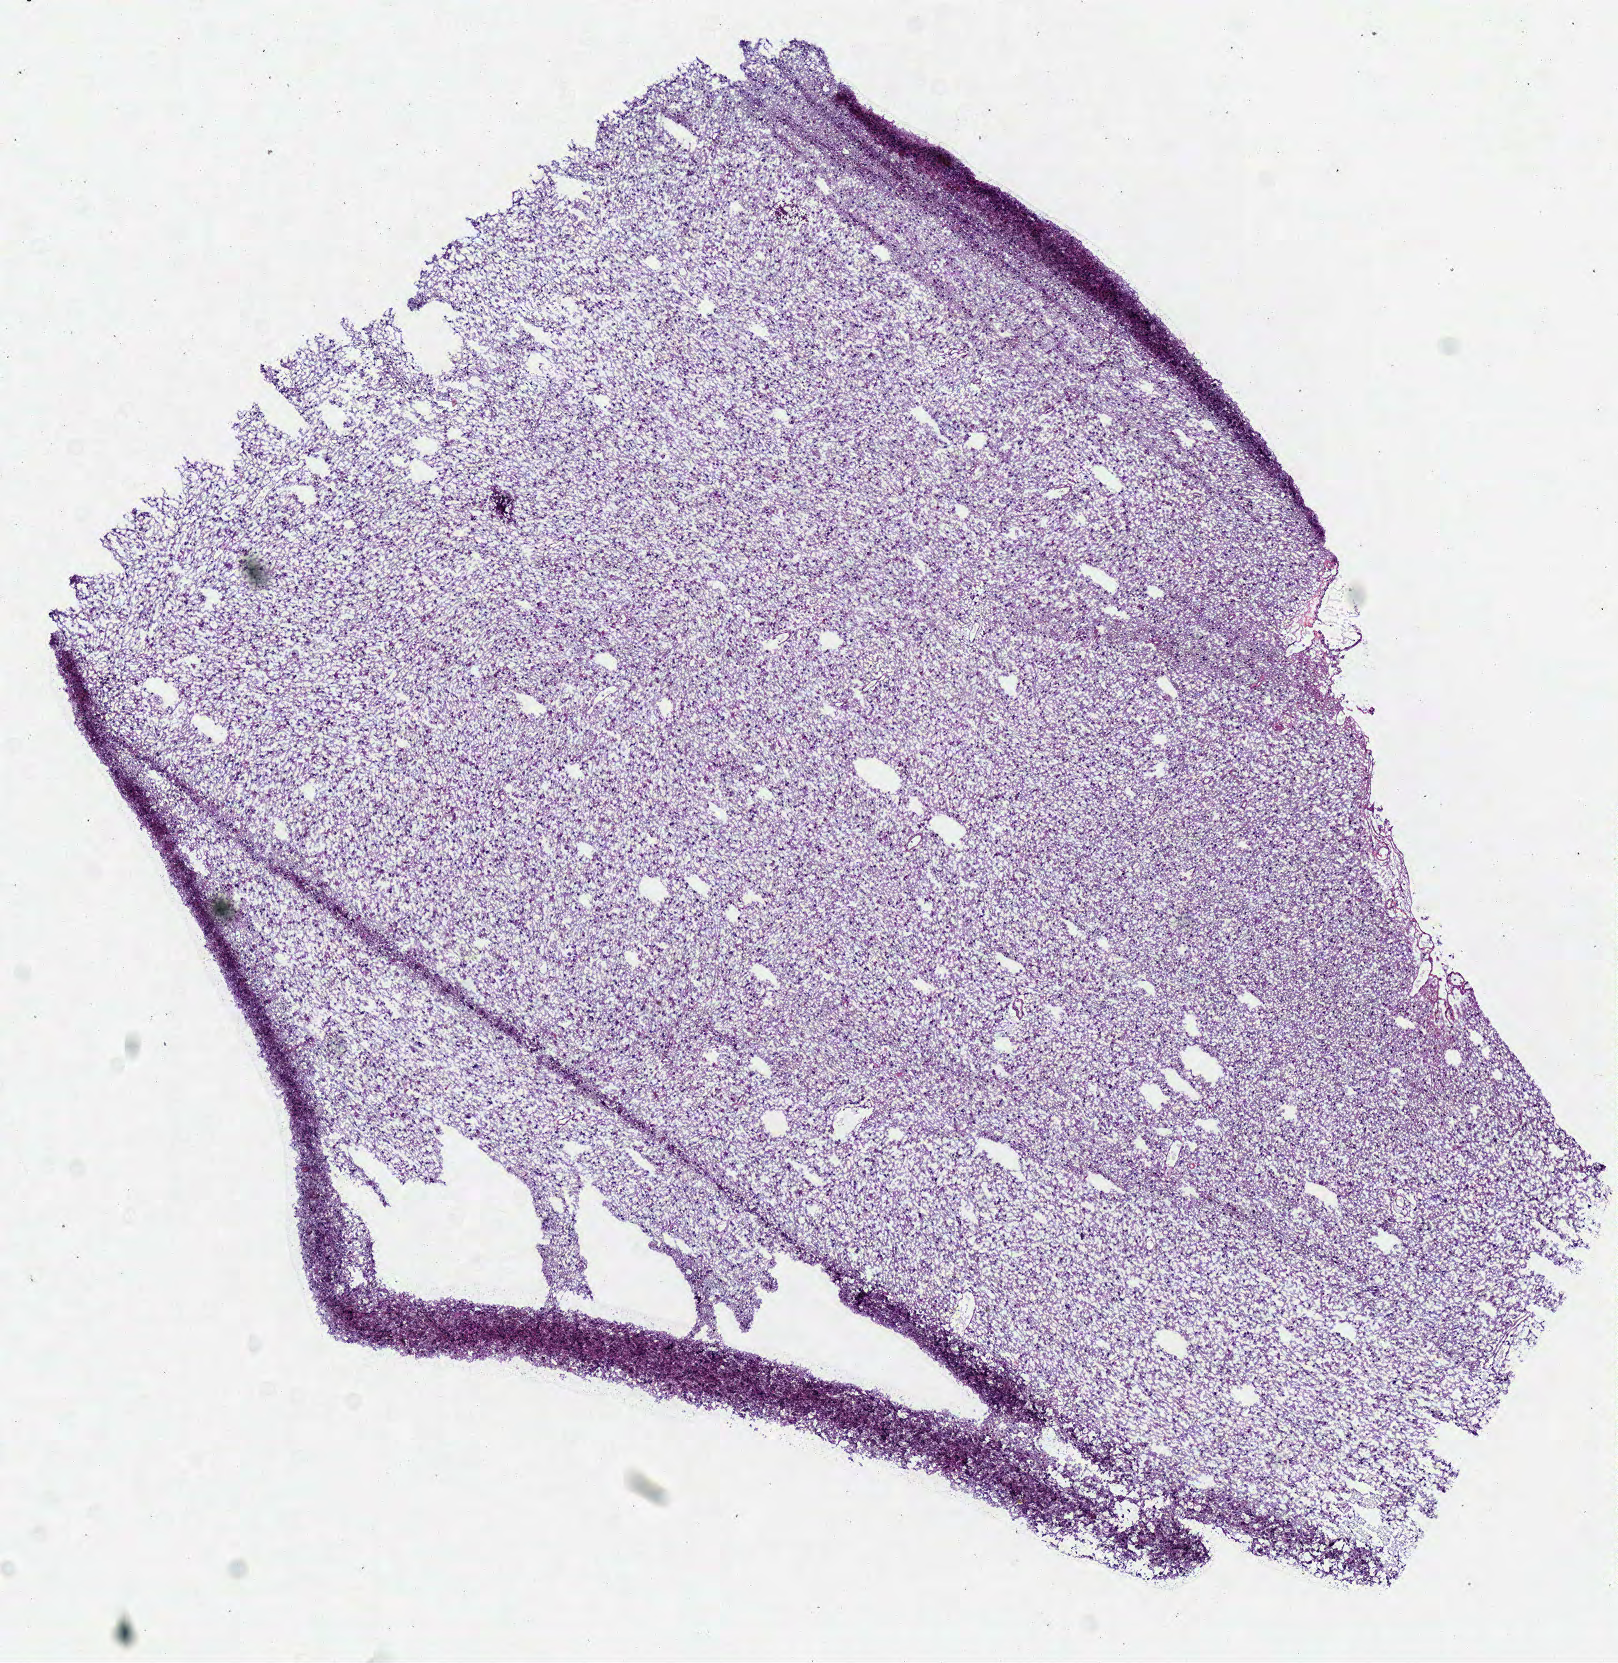
Whole-slide histology image, H&E — a low-resolution overview of the entire scanned area, about 6.4 x 6.5 mm (from a 40x scan); frozen section; brain, primary tumour sample. Female, age 39 years at initial diagnosis. Histologic grade: G2 (moderately differentiated). Slide review estimates, as recorded: tumour cells 100%, tumour nuclei 65%, normal cells 0%, stromal cells 0%, necrosis 0%.
Diagnosis: Mixed glioma (cerebrum). Laterality: right.